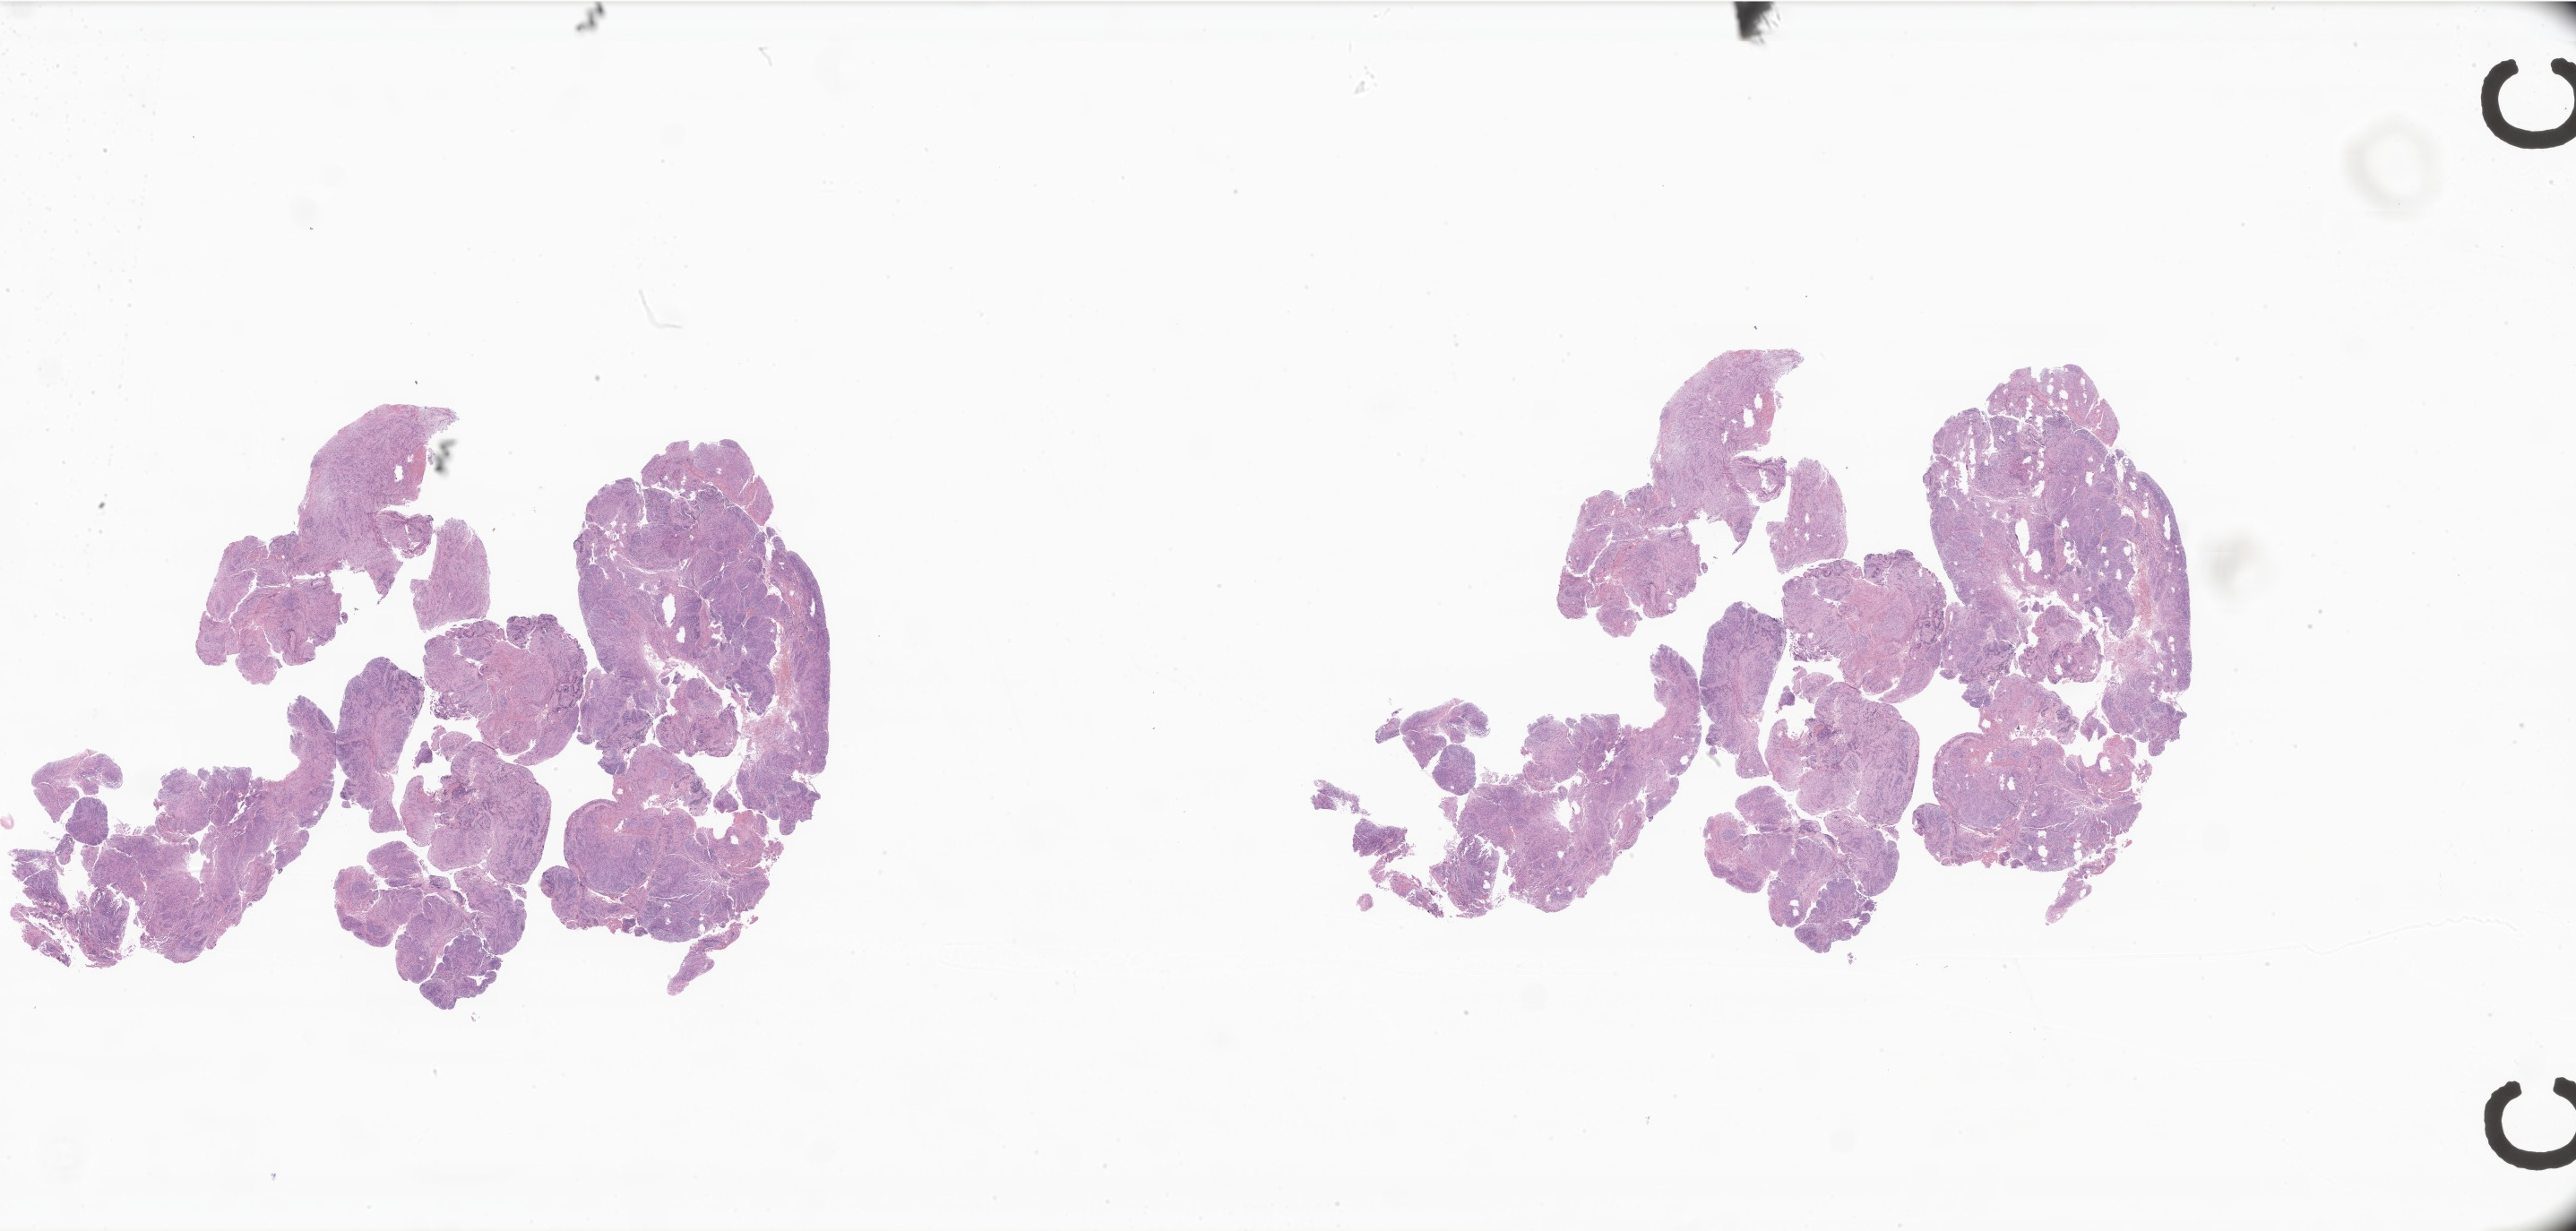
Whole-slide image, H&E stain of tumor tissue from the spinal cord, a low-resolution overview of the entire scanned area, about 48.5 x 23.2 mm; formalin-fixed, paraffin-embedded (FFPE) tissue. Patient female; age 156 months (13 years).
* diagnosis (ICD-O-3 morphology term): Neoplasm, uncertain whether benign or malignant